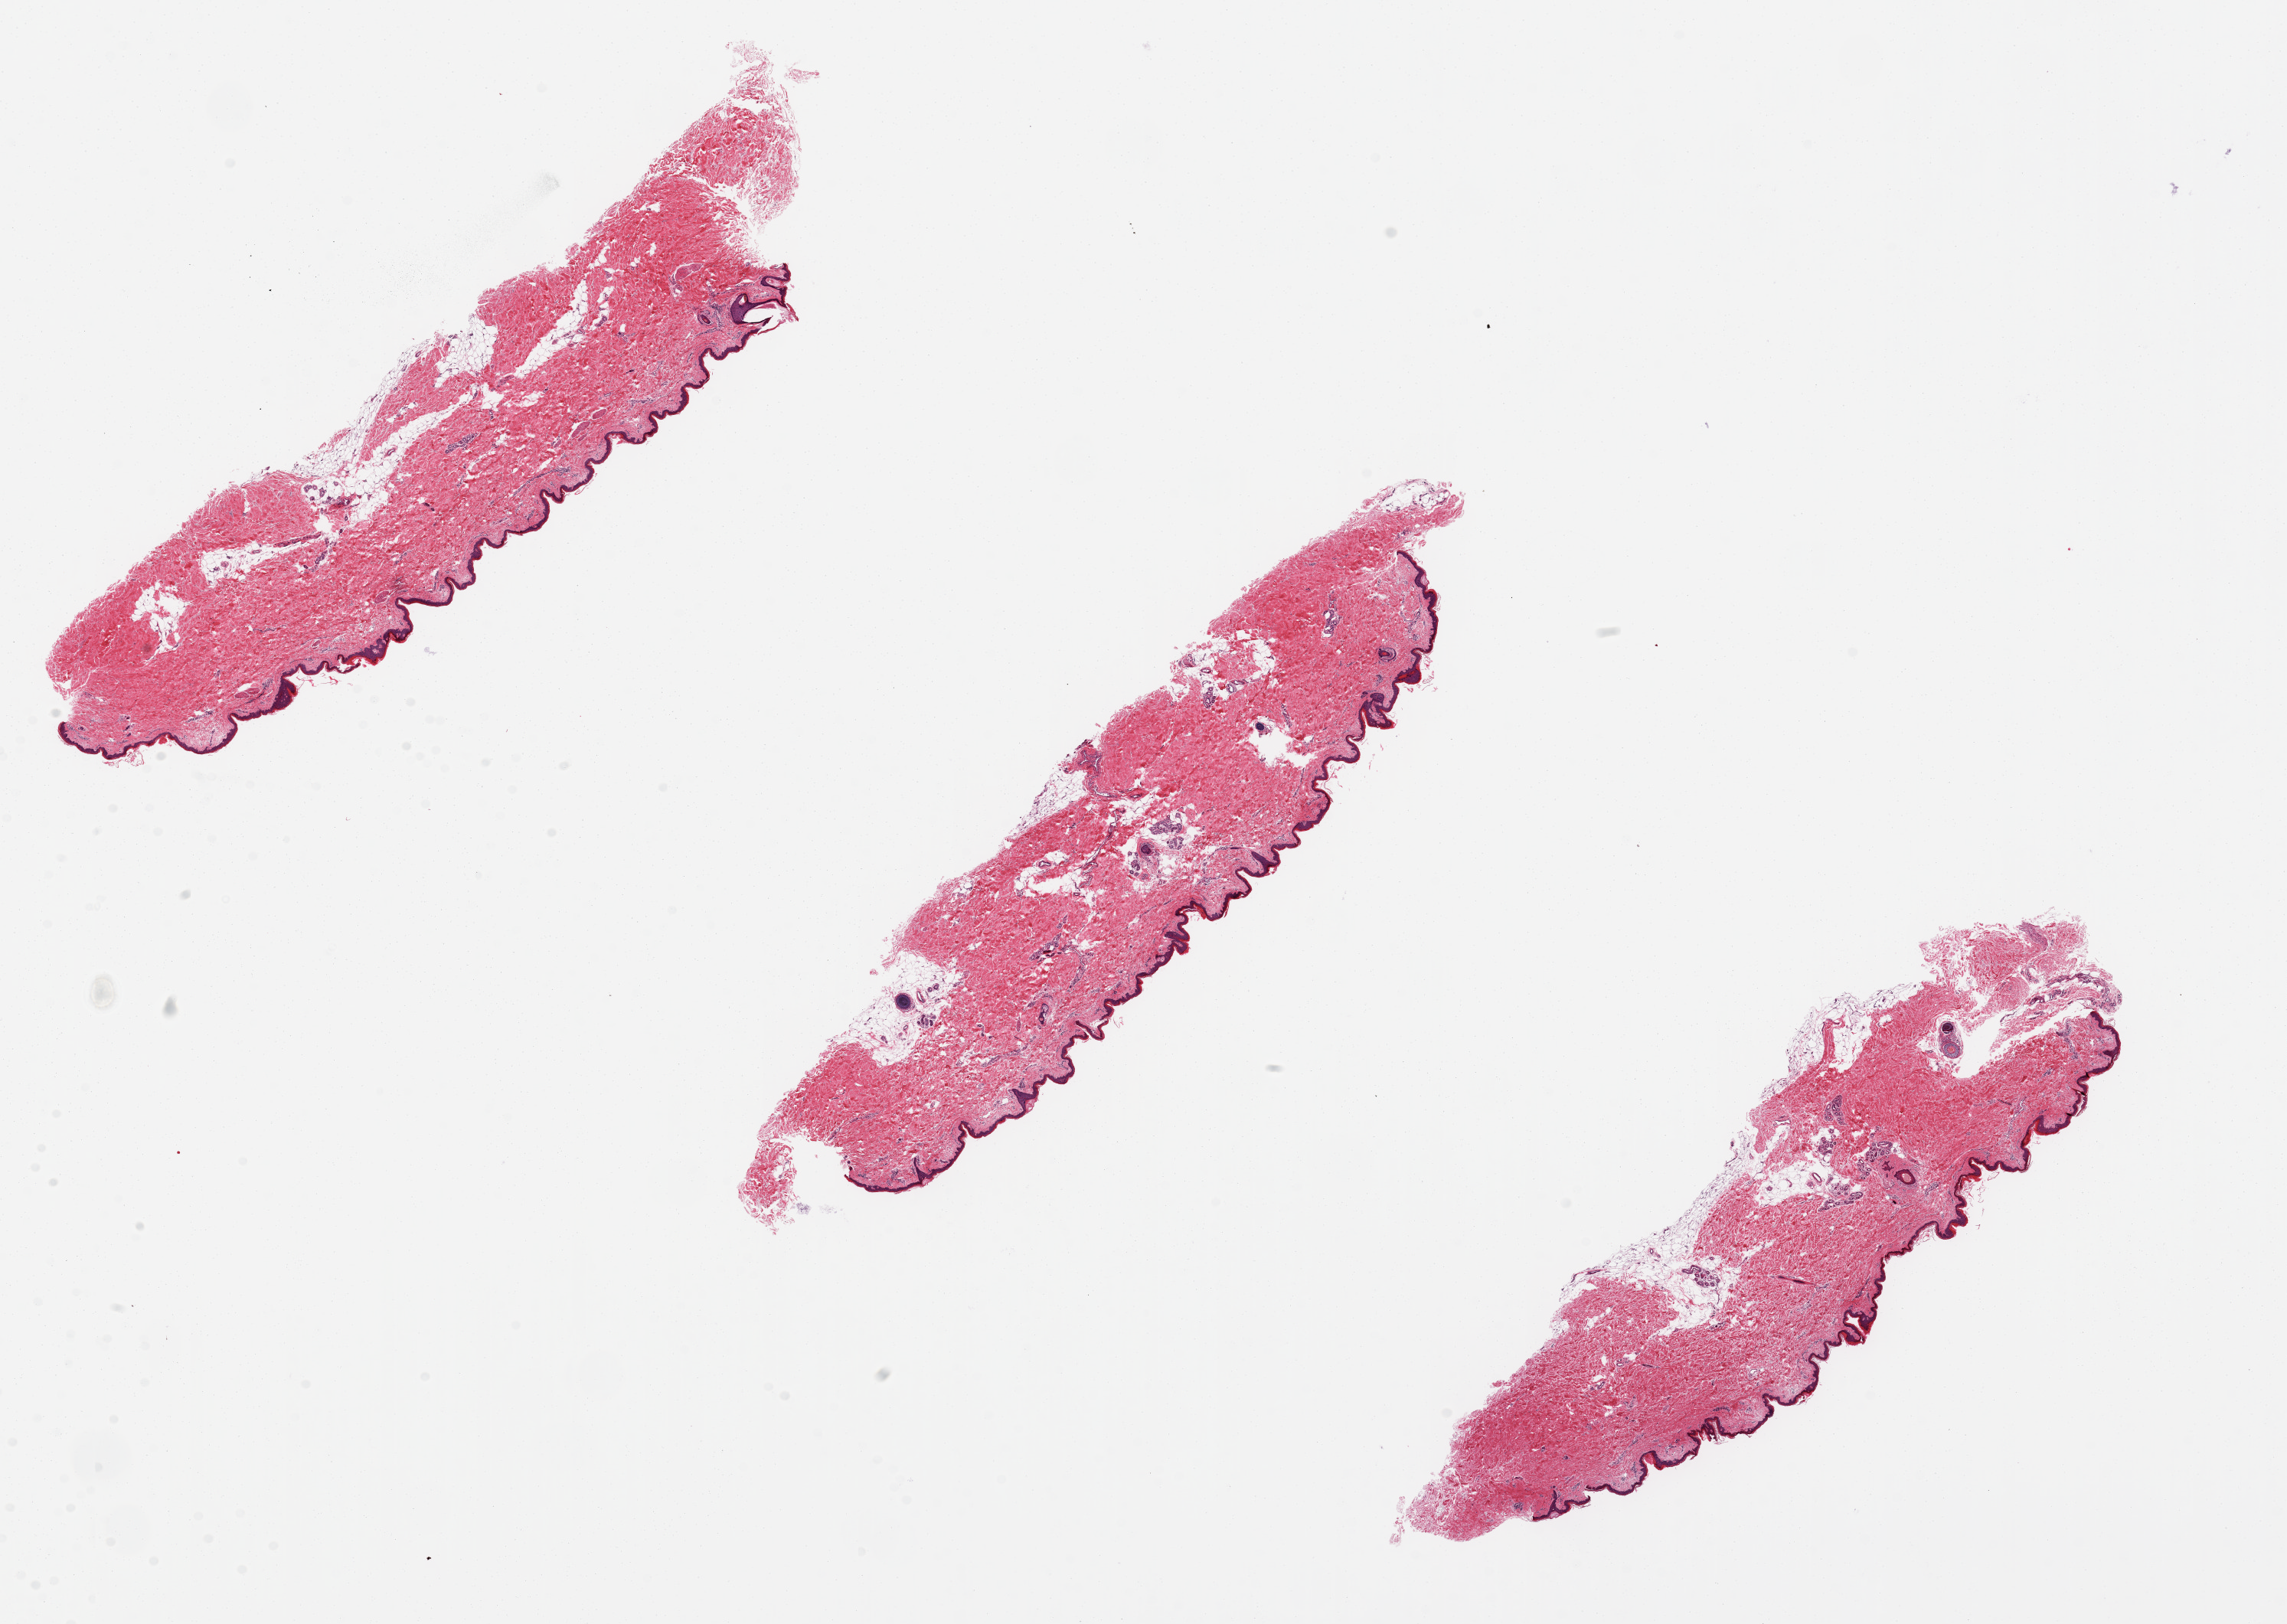
Hematoxylin and eosin (H&E) whole-slide image, a low-resolution overview of the entire scanned area, about 23.6 x 16.8 mm (acquisition: 20x scan). PAXgene-fixed paraffin-embedded (PFPE) section. Sampled site (target tissue): skin of lower leg. Tissue donor sample. Donor: male.
Reviewer comment on this tissue sample: 3 ~9x2mm pieces. Epithelium is ~1% or less of specimen thickness. Areas of poor fixation with tears/holes in dermis.